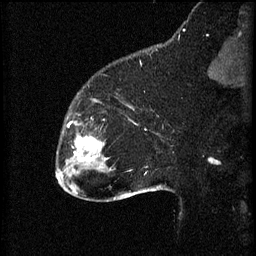
Breast MRI (dynamic contrast-enhanced), one sagittal slice. Position 15 of 60 along the scan axis. 3 images stored at this slice position (order not interpretable as contrast timing). 1.5 T. TE 4.2 ms, TR 8.2 ms. 256 × 256 image matrix, field of view 180 × 180 mm. Patient: female, 32 years.
Annotated regions visible in this slice (semi-automatically segmented with operator editing):
- analysis volume of interest (the breast-tissue region the enhancement analysis was run in; not a lesion): box from (x=58, y=114) to (x=110, y=165) px
- tumour enhancement mask (voxels above the 70 % enhancement threshold inside the analysis volume of interest): (x=67, y=126)–(x=101, y=163)